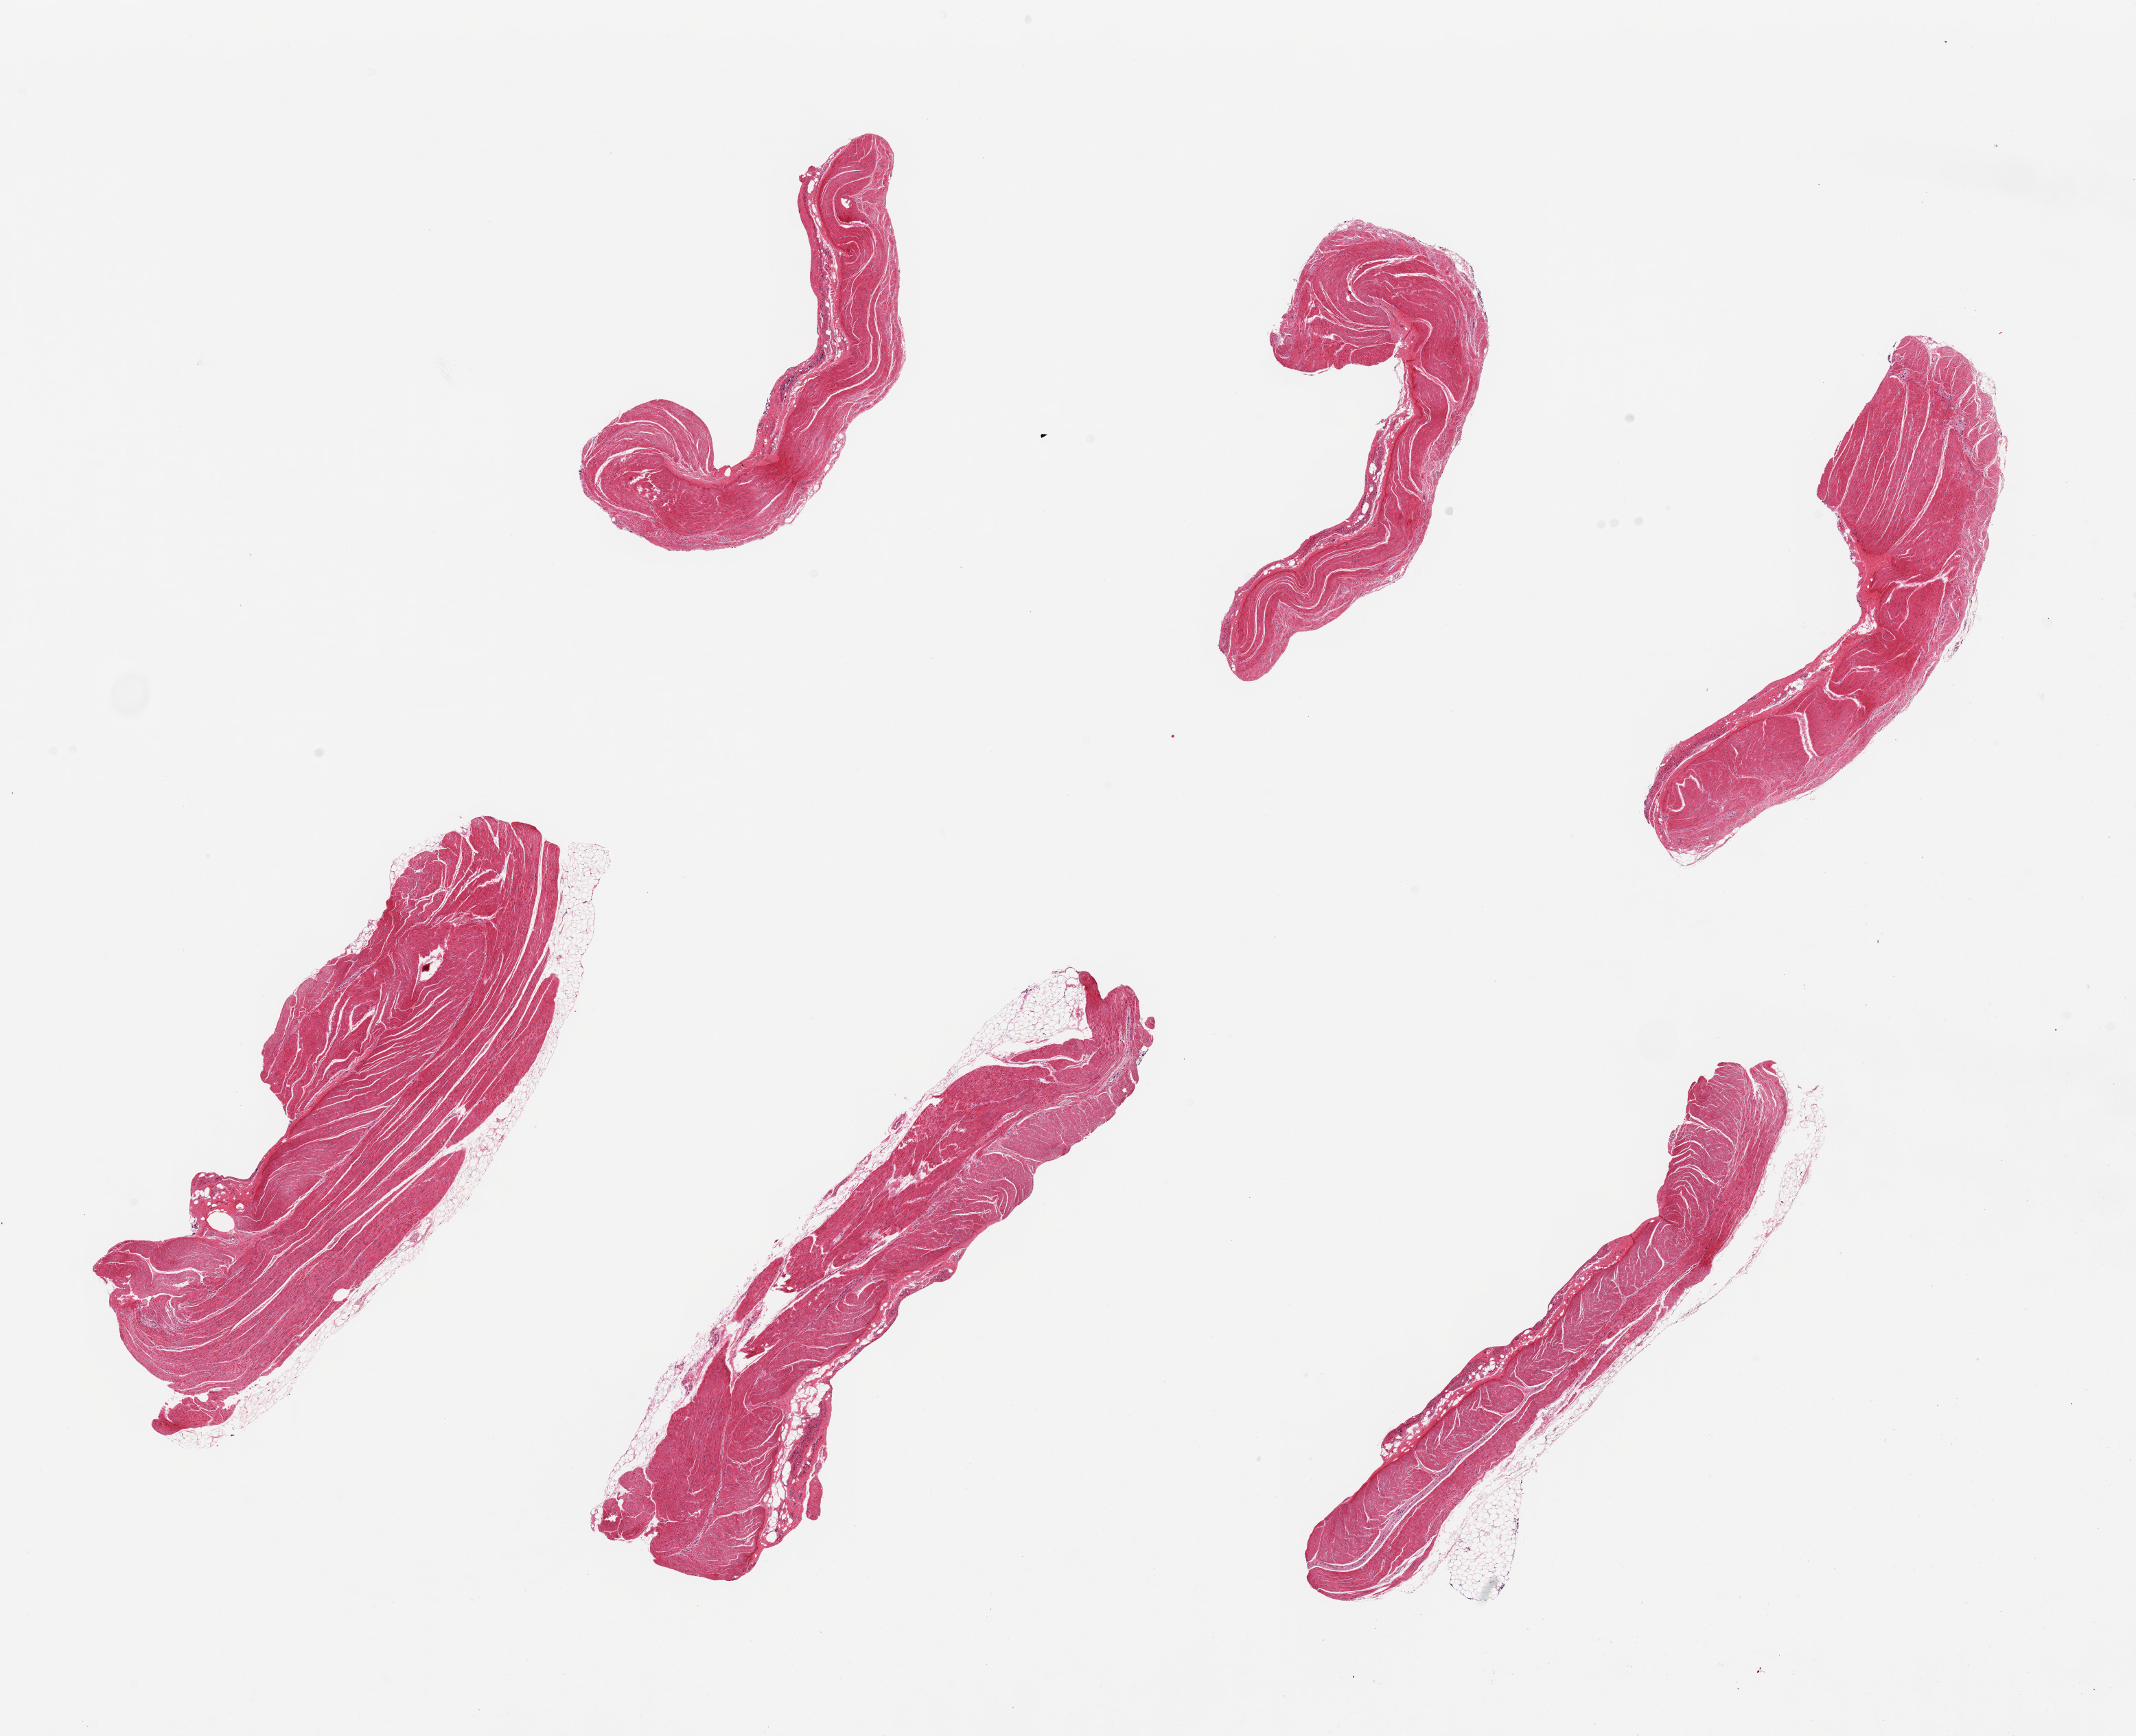
Digitized hematoxylin and eosin (H&E)-stained section — shown as a low-resolution overview of the whole scanned area (about 24.6 x 20.0 mm, from a 20x scan); PAXgene-fixed paraffin-embedded (PFPE) section; sampled site (target tissue): sigmoid colon; donor tissue sample. Male donor.
• pathologist's review note for this sample: 6 pieces. well dissected muscularis